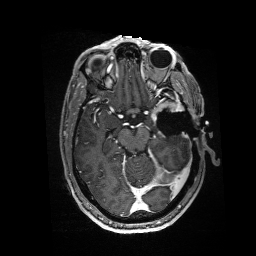
Brain MRI from a brain-tumour surgery series, one axial slice. Slice 100 of 176 in the series (ordered by position). T1-weighted post-contrast. 1 mm slice thickness. 256 × 256 image matrix, field of view 256 × 256 mm. Case-level facts recorded for this patient, not image findings: histopathology: Glioblastoma; WHO grade: 4; IDH mutation: no.
Outlined on this slice (manually delineated by an expert):
- residual tumour: box from (x=151, y=101) to (x=185, y=122) px